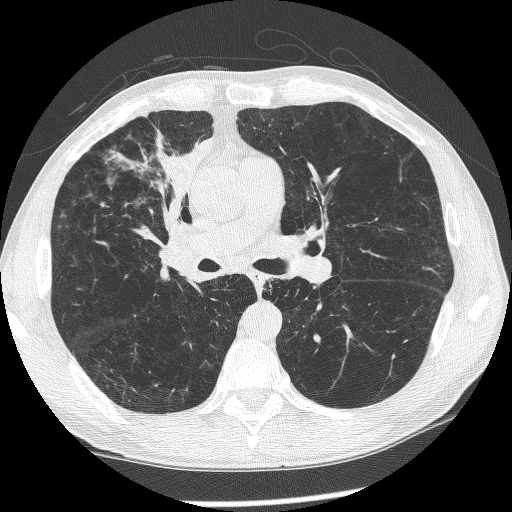
Low-dose screening chest CT, axial slice; first (baseline) screen; lung window (W 1500 / L -600 HU); 1.25 mm slice thickness; slice 140 of 266 in the series. Male, age 60 years at enrolment.
Expert reader's lesion annotation, box from (x=145, y=183) to (x=217, y=277) px. The exam's reader record, not a measurement of the box and not confirmed to be the same lesion: non-calcified nodule or mass ≥4 mm, right upper lobe, 12 × 8 mm, spiculated (stellate) margins, mixed attenuation. Official screen result: positive, change unspecified: nodule(s) >= 4 mm or enlarging nodule(s), mass(es), or other non-specific abnormalities suspicious for lung cancer. Participant outcome: lung cancer diagnosed 208 days after this screen — squamous cell carcinoma, NOS, right upper lobe, right middle lobe, right main stem bronchus, poorly differentiated (G3), stage IV (AJCC 6th edition).